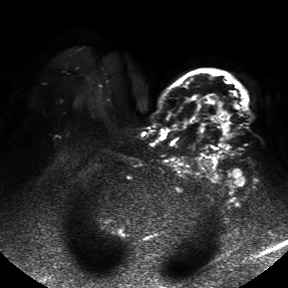
Breast MRI, one axial slice; position 34 of 50 along the scan axis; diffusion-weighted series; image 2 of 4 stored at this slice position (different b-values; order by instance number); 1.5 T; 4 mm slice thickness; 288 × 288 image matrix. Female patient.
Outlined on this slice (outlined manually by an expert reader):
- tumour on diffusion-weighted imaging: bounding box (x1, y1, x2, y2) in pixels: (217, 121, 231, 148)